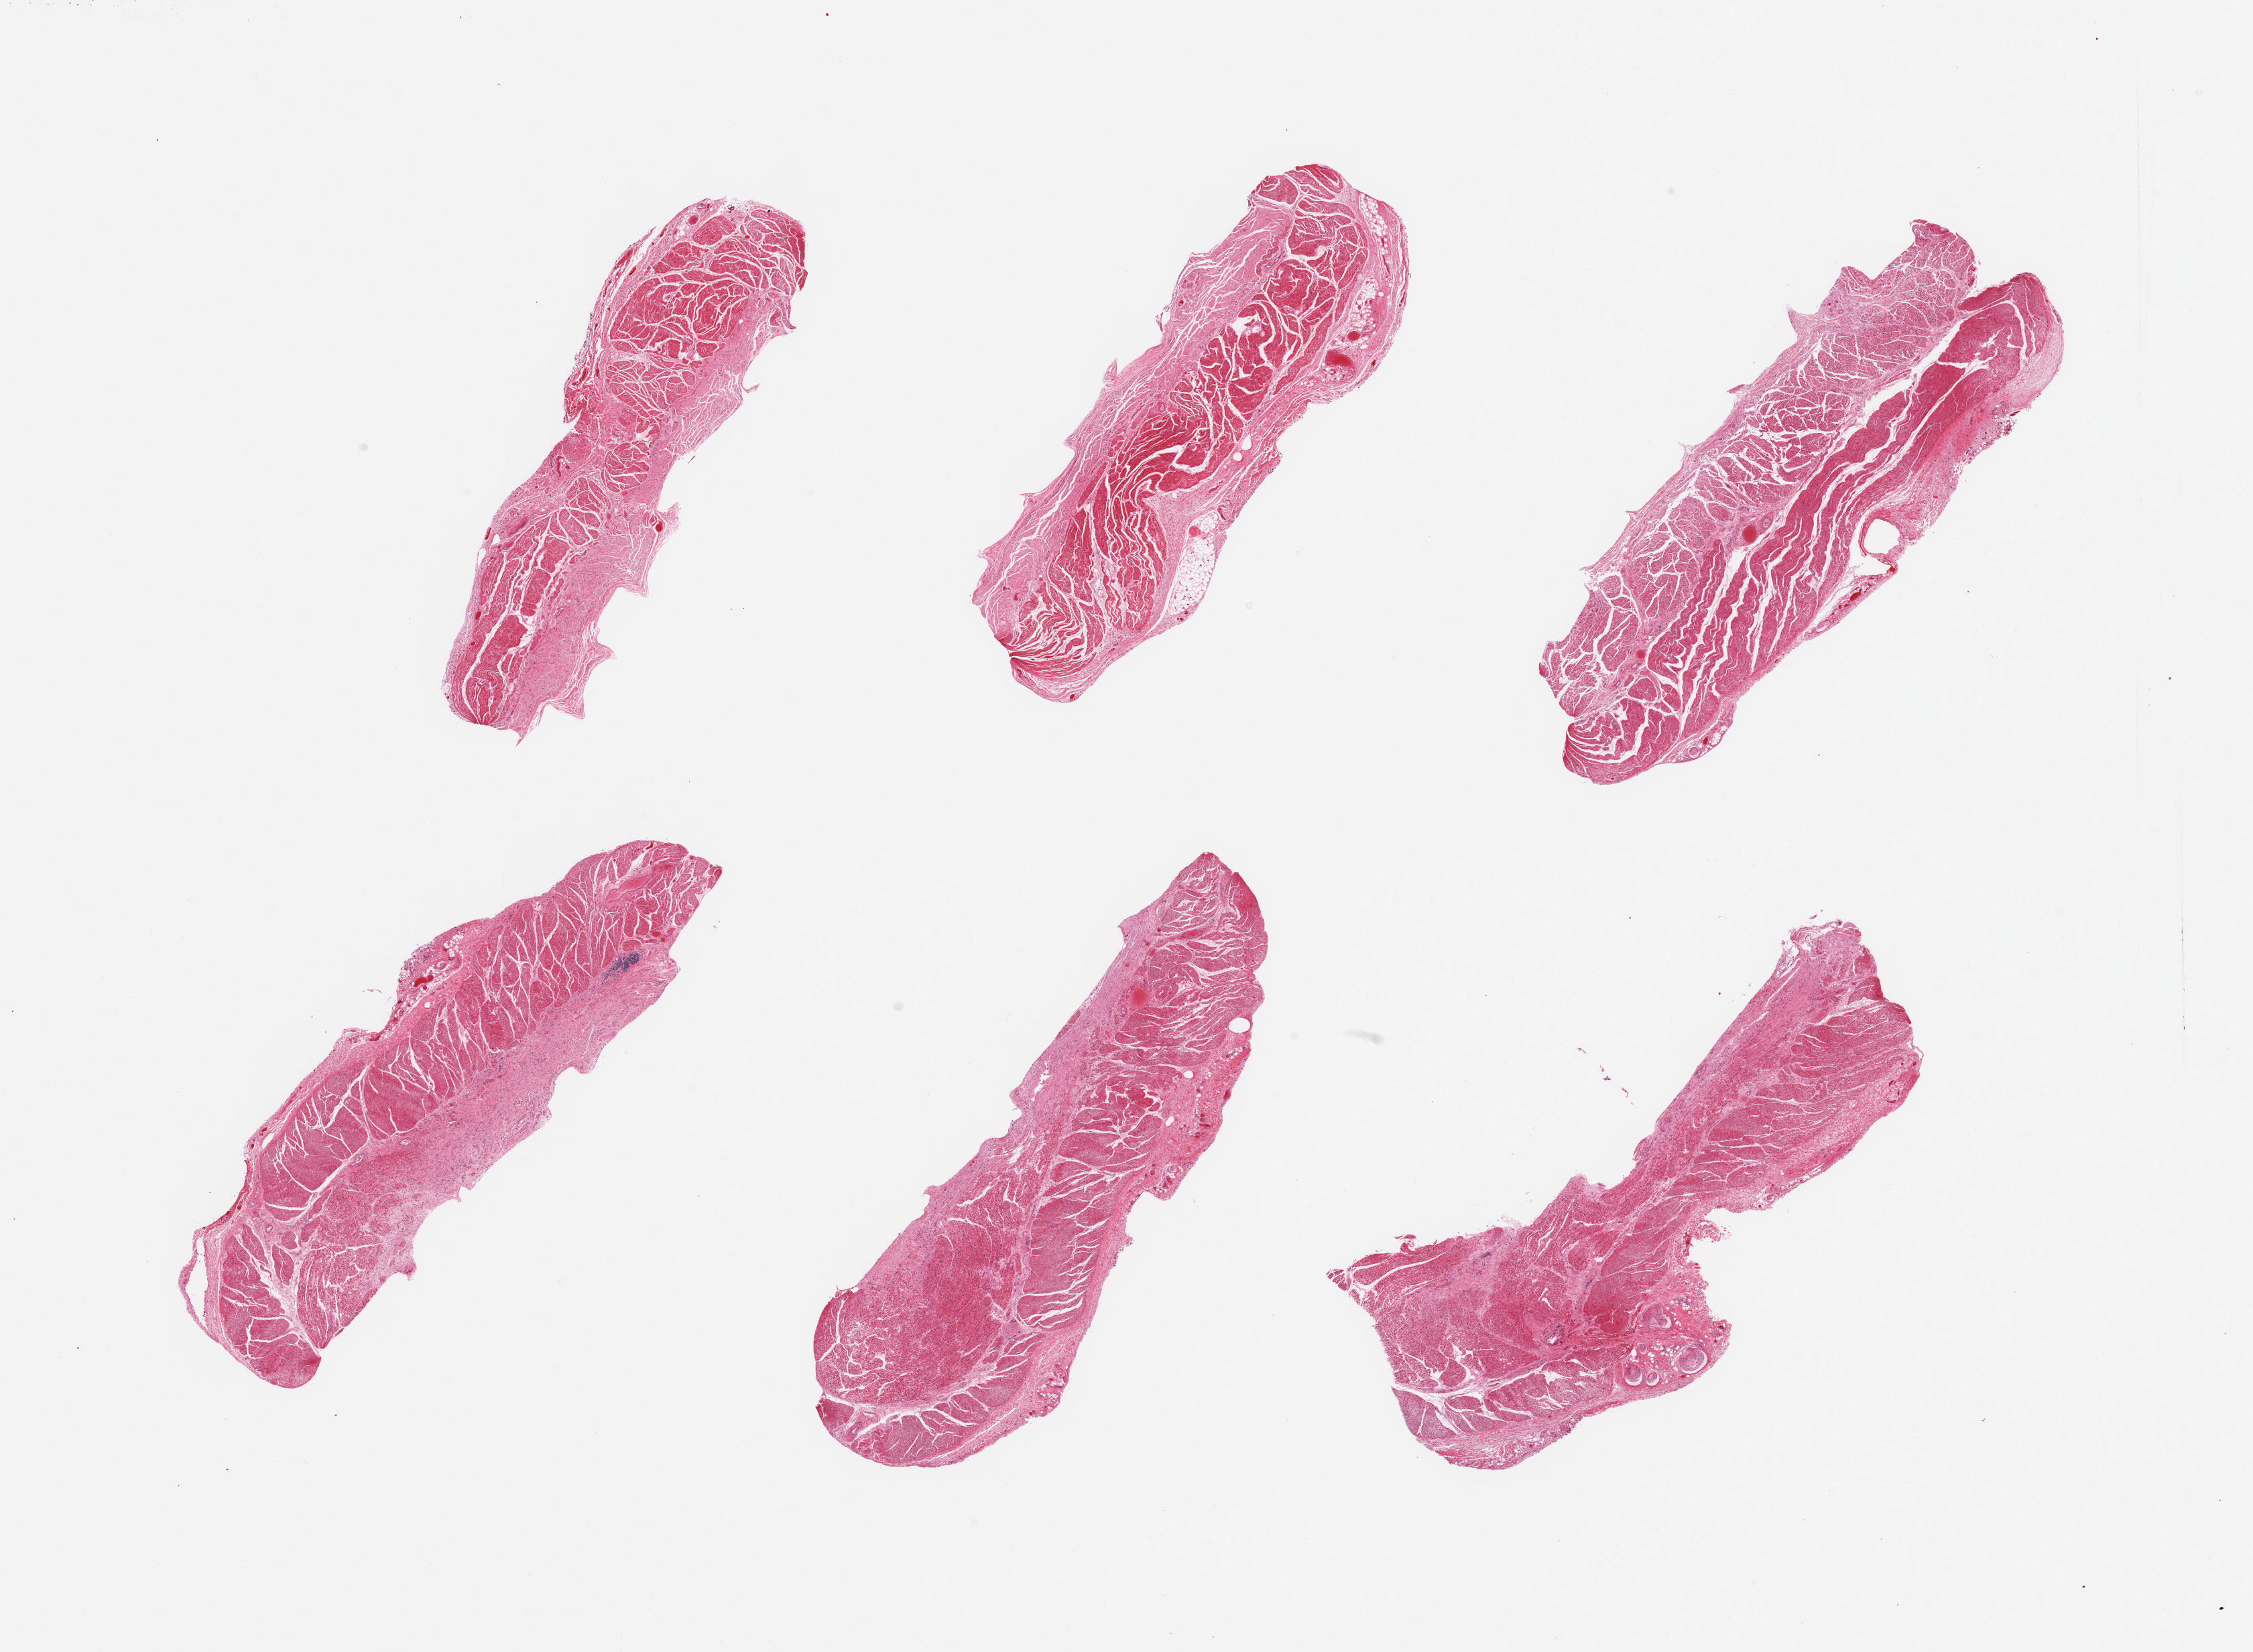
Haematoxylin and eosin whole-slide image, a low-resolution overview of the entire scanned area, about 26.6 x 19.5 mm, PAXgene-fixed paraffin-embedded (PFPE) section, section of esophageal muscle (target tissue), donor tissue sample. Donor sex: male.
Review note (as recorded): 6 pieces; submucosal and adventitial stroma account for up to 30% content.